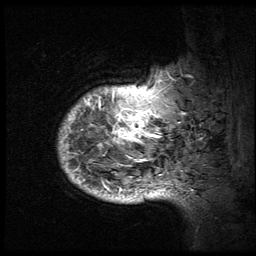
Breast MRI (dynamic contrast-enhanced), one sagittal slice. Position 9 of 64 along the scan axis. 3 images stored at this slice position (order not interpretable as contrast timing). 1.5 T. TE 4.2 ms, TR 9 ms. 2.5 mm slice thickness. 256 × 256 image matrix. Female patient, age 50 years. From the clinical record (not read from this slice): setting: breast cancer imaged before/during neoadjuvant chemotherapy; receptor status: triple-negative.
Outlined on this slice (semi-automatic segmentation, software-assisted and operator-edited):
- analysis volume of interest (the breast-tissue region the enhancement analysis was run in; not a lesion): bounding box <59,43,194,212> (left, top, right, bottom; pixels)
- tumour enhancement mask (voxels above the 140 % enhancement threshold inside the analysis volume of interest): <59,68,194,202>